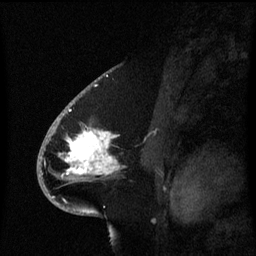
Breast MRI (dynamic contrast-enhanced), one sagittal slice; position 39 of 60 along the scan axis; dynamic contrast-enhanced series, image 2 of 3 at this slice position (ordered by acquisition); 1.5 T; TE 4.2 ms, TR 8.4 ms; 256 × 256 image matrix, field of view 200 × 200 mm. Female patient, age 53 years. Case-level facts recorded for this patient, not image findings: setting: breast cancer imaged before/during neoadjuvant chemotherapy; receptor status: HR-positive, HER2-negative.
Outlined on this slice (semi-automatic segmentation, software-assisted and operator-edited):
- analysis volume of interest (the breast-tissue region the enhancement analysis was run in; not a lesion): bounding box <49,108,124,201> (left, top, right, bottom; pixels)
- tumour enhancement mask (voxels above the 70 % enhancement threshold inside the analysis volume of interest): <60,130,120,175>